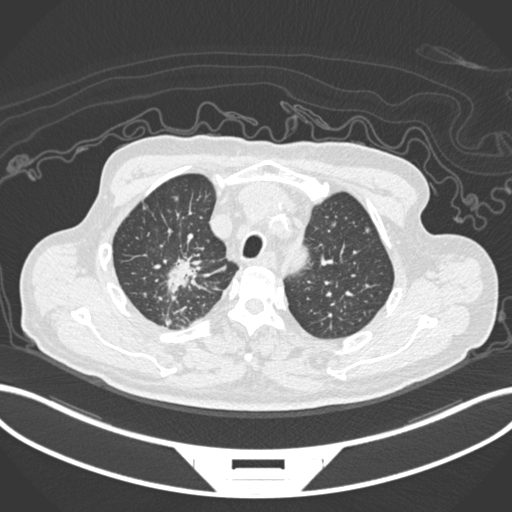
Chest CT, one axial slice; reconstruction kernel B30f; lung window (W 1500 / L -600 HU); 1 mm slice thickness; 512 × 512 image matrix, field of view 400 × 400 mm. Male patient, age 69 years. From the clinical record (not read from this slice): clinical TNM (as recorded): T1c N1 M1.
Annotated regions visible in this slice (rectangle marked by the reading radiologist):
- lung tumour (recorded histology: adenocarcinoma): box from (x=158, y=249) to (x=202, y=303) px